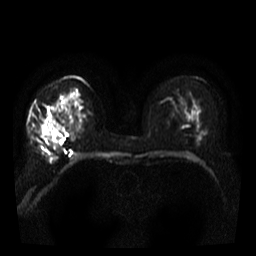
Breast MRI, one axial slice; diffusion-weighted series; image 2 of 4 stored at this slice position (different b-values; order by instance number); 3 T; 5 mm slice thickness; 256 × 256 image matrix, field of view 300 × 300 mm. Female patient.
Structures marked on this image (expert manual segmentation):
- tumour on diffusion-weighted imaging: bounding box [x1, y1, x2, y2] px = [38, 130, 62, 147]